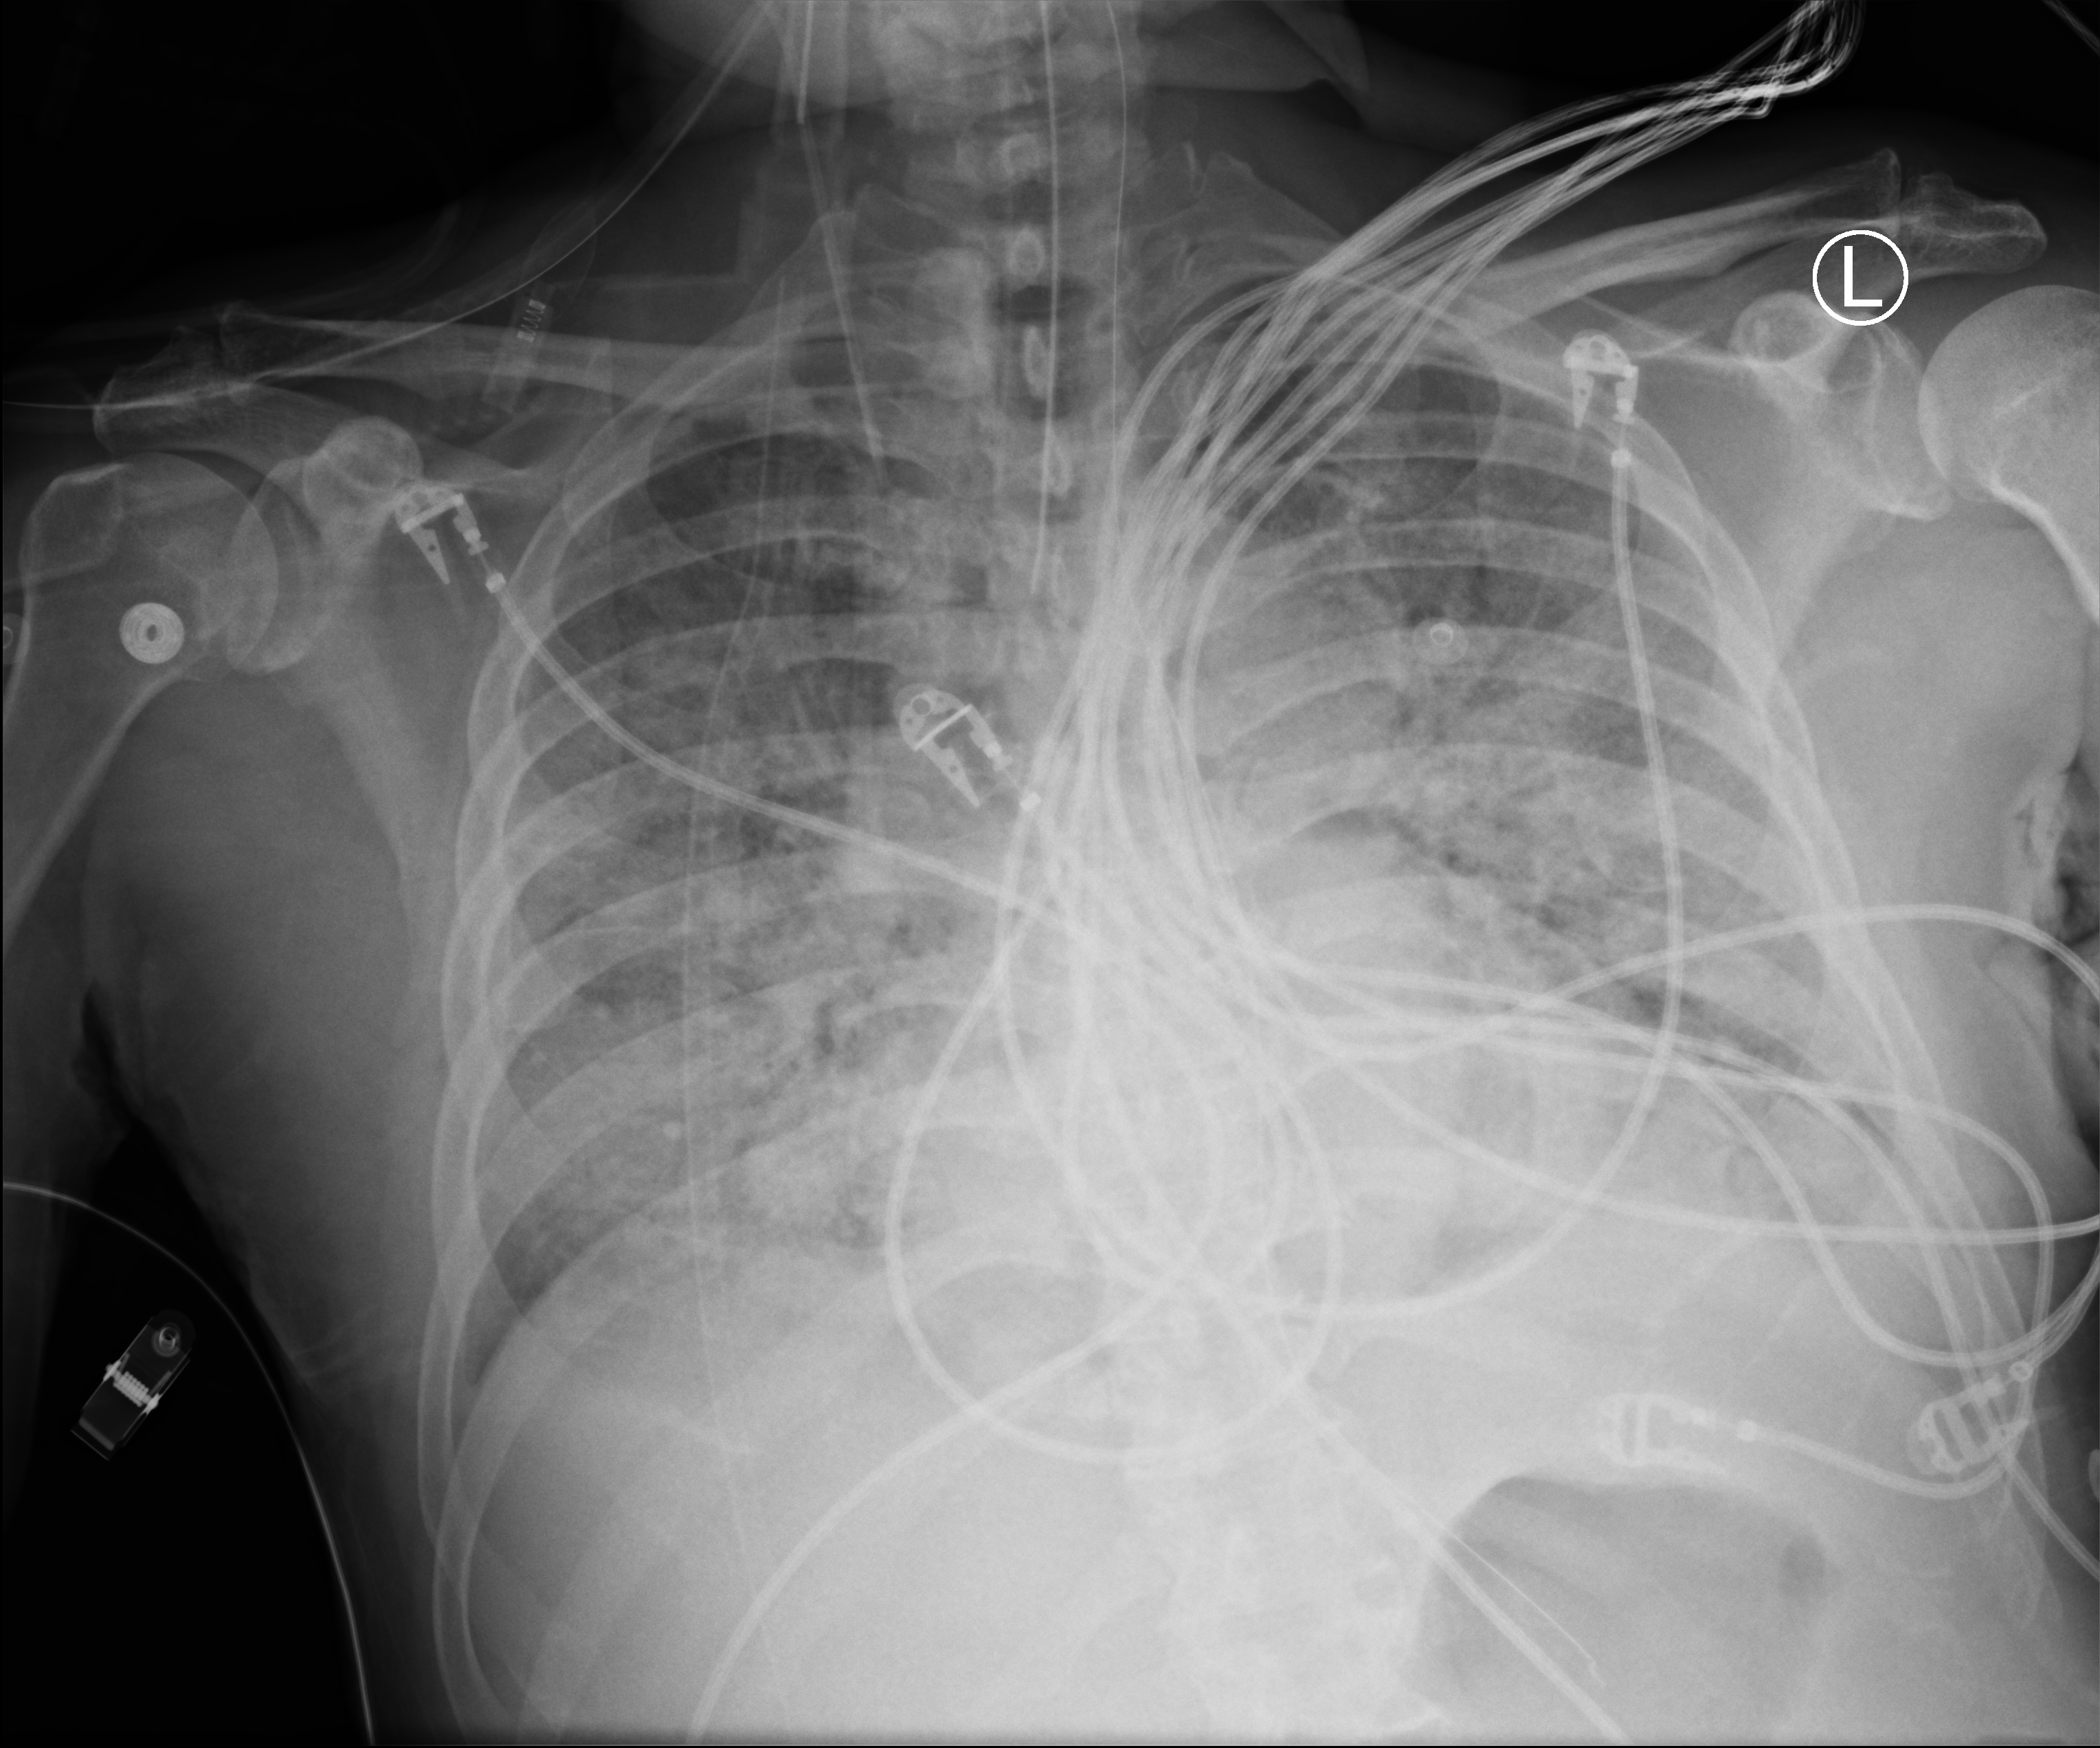
Portable chest radiograph; anteroposterior (AP) projection. Male patient hospitalised with COVID-19, age 60–74 years.
Hospital-stay facts (about this admission, not read from this image; timing relative to this image not recorded):
- COPD (admission record): no
- mechanically ventilated during this hospital stay: yes
- admitted to intensive care during this hospital stay: yes